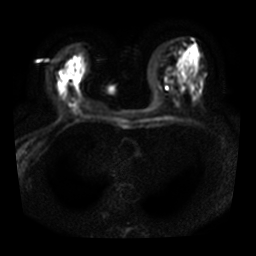
Breast MRI, one axial slice; position 15 of 28 along the scan axis; diffusion-weighted series; image 2 of 4 stored at this slice position (different b-values; order by instance number); 3 T; 5 mm slice thickness; 256 × 256 image matrix, field of view 320 × 320 mm. Female patient.
Annotated regions visible in this slice (outlined manually by an expert reader):
- tumour on diffusion-weighted imaging: box from (x=62, y=69) to (x=68, y=73) px